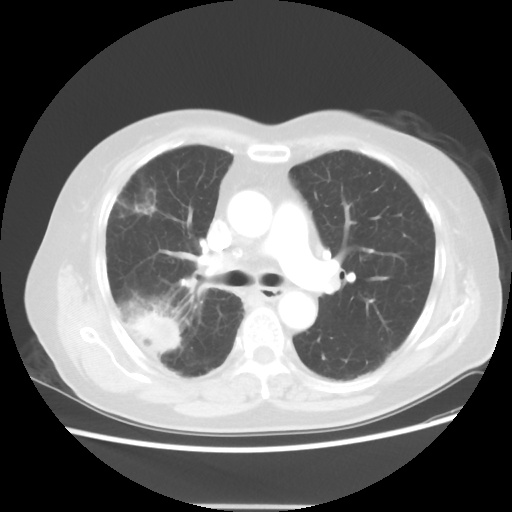
Chest CT, one axial slice. Slice 30 of 50 in the series (ordered by position). Reconstruction kernel STANDARD. 120 kVp. Lung window (W 1500 / L -600 HU). 512 × 512 image matrix, field of view 360 × 360 mm. Patient: female, 72 years. From the clinical record (not read from this slice): clinical TNM (as recorded): T2 N1 M0; histopathological grade: G1.
Annotated regions visible in this slice (rectangle marked by the reading radiologist):
- lung tumour (recorded histology: adenocarcinoma): bounding box <130,310,180,350> (left, top, right, bottom; pixels)